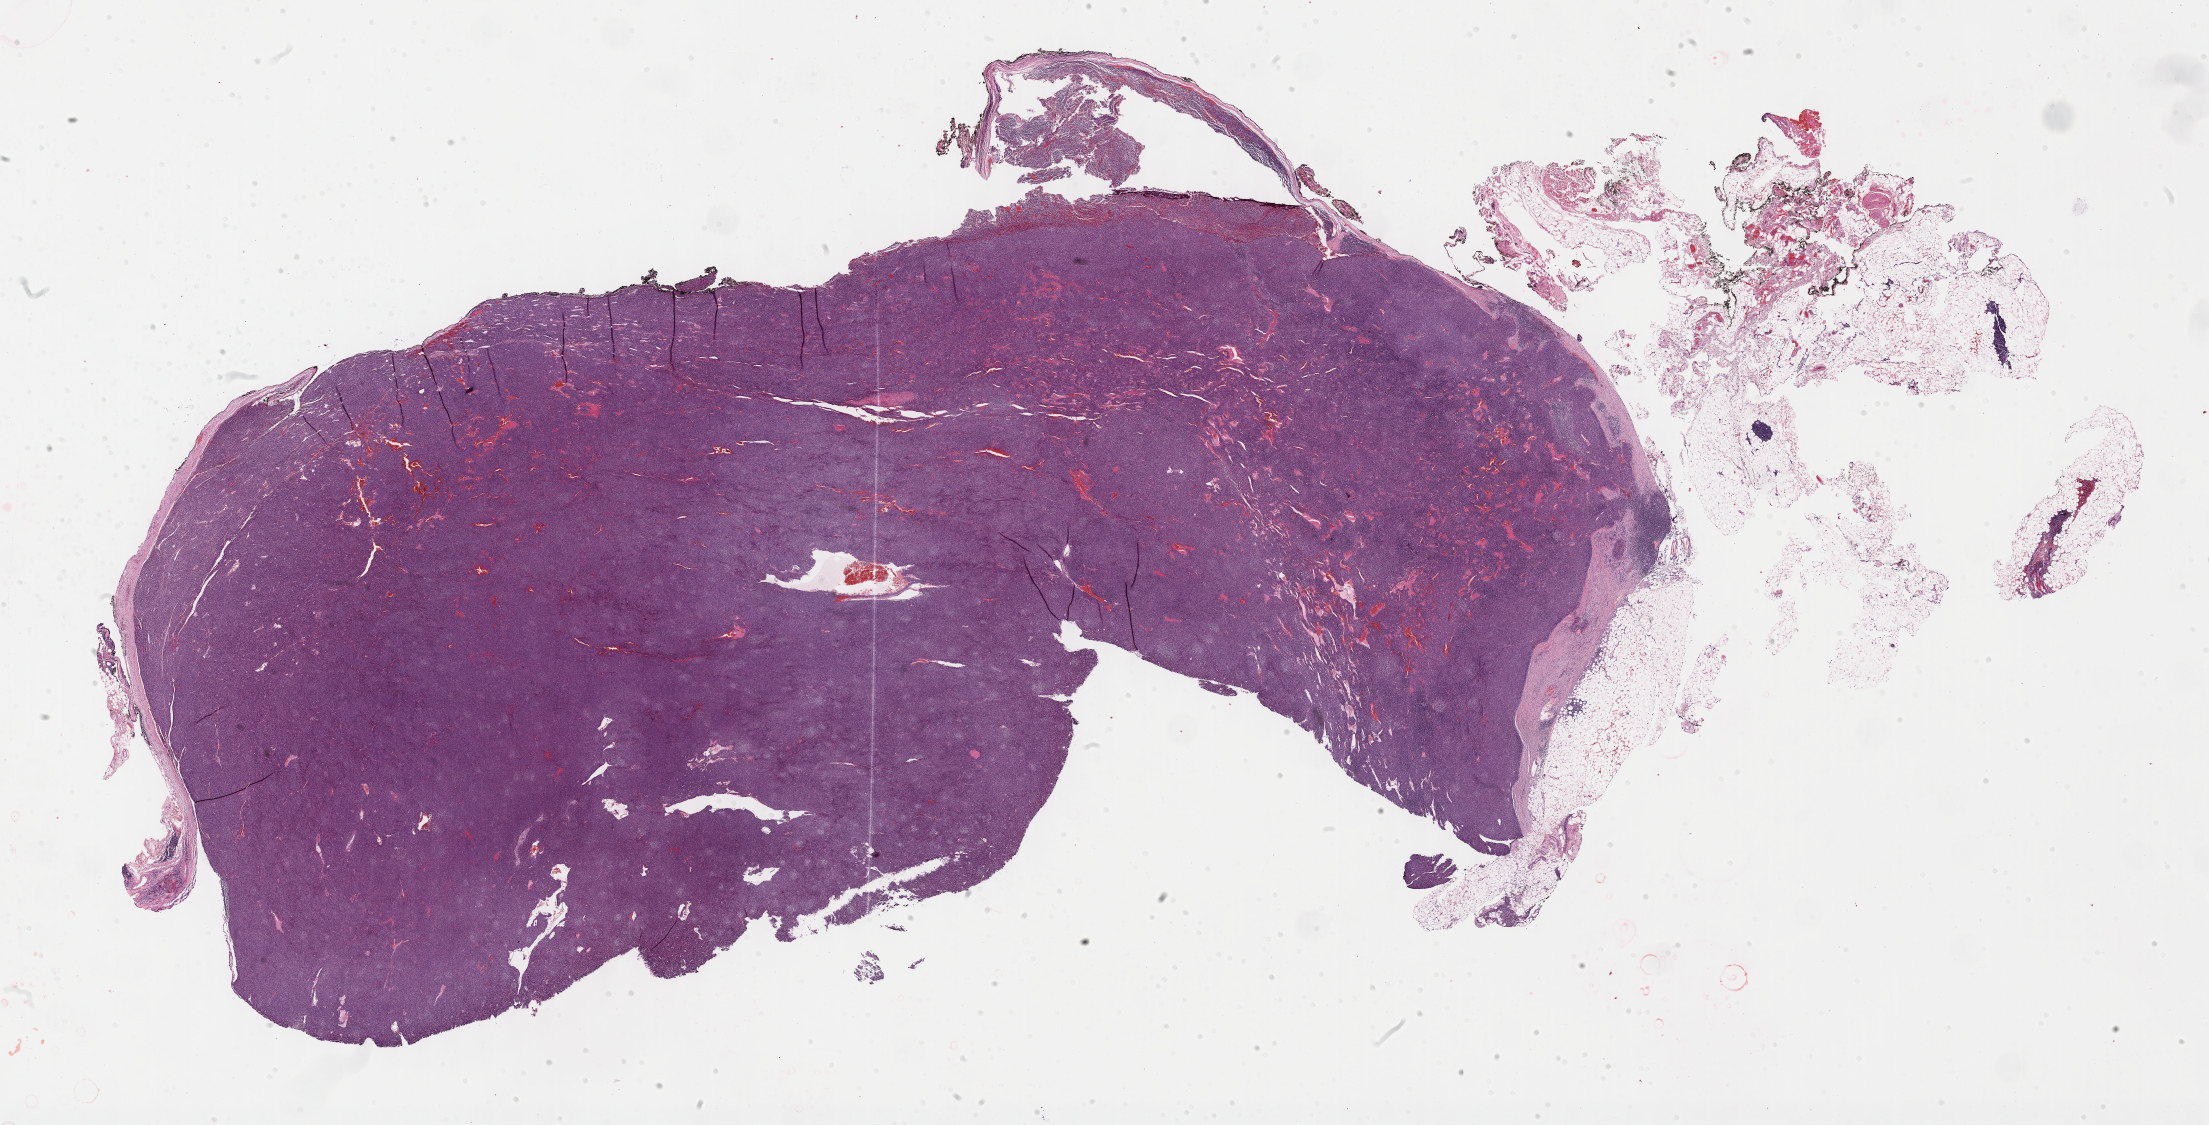
Hematoxylin and eosin (H&E) stained whole-slide image — low-resolution overview of the scanned area, about 35.7 x 18.2 mm; formalin-fixed paraffin-embedded (FFPE) diagnostic section; sample: primary tumour, thymus. Female, age 84 years at initial diagnosis.
- pathologic diagnosis: Thymoma, type A, malignant (anterior mediastinum)